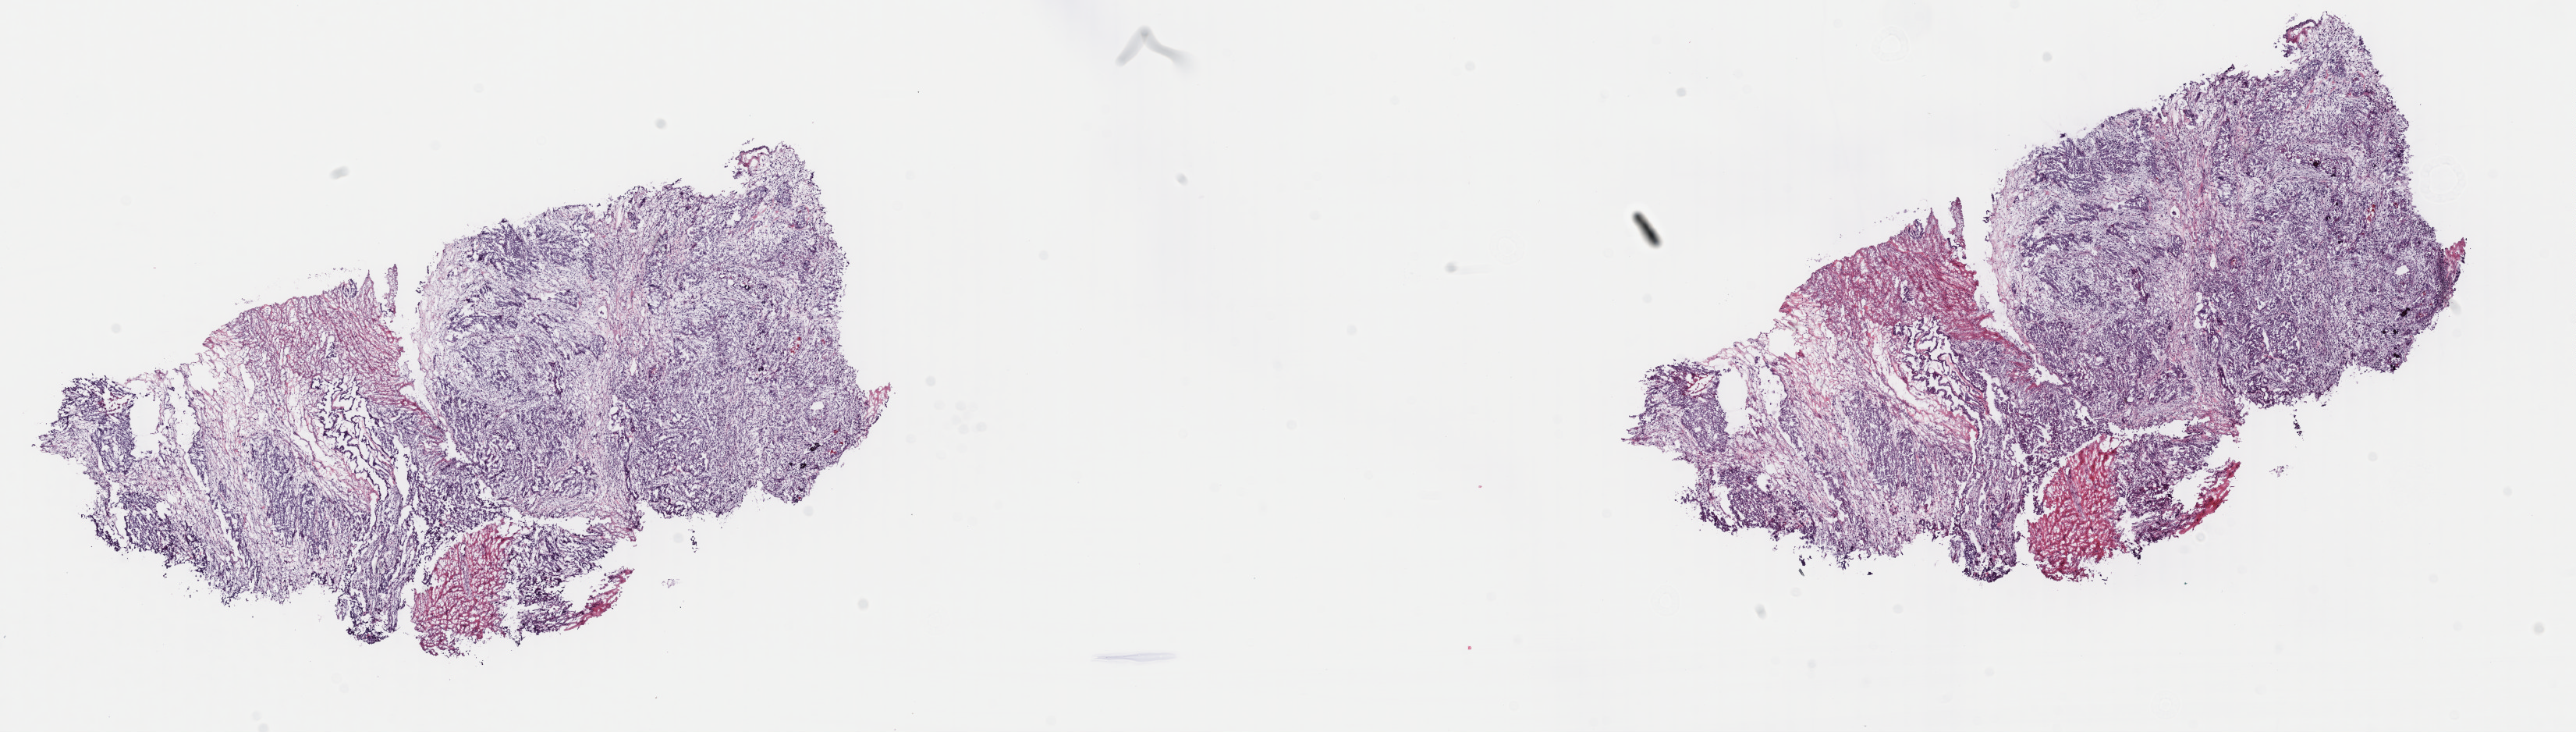
Hematoxylin and eosin (H&E) stained whole-slide image, shown as a low-resolution overview of the whole scanned area (about 26.0 x 7.4 mm, from a 40x scan); frozen section from the top of the tissue portion; primary tumour sample from the uterus. Female, age 75 years at initial diagnosis. Slide review estimates, as recorded: tumour cells 70%, tumour nuclei 70%, normal cells 0%, stromal cells 20%, necrosis 10%. Infiltration values recorded for this section: lymphocyte infiltration 40%, monocyte infiltration 20%, neutrophil infiltration 20%.
• FIGO stage: IB
• histologic diagnosis: Mullerian mixed tumor